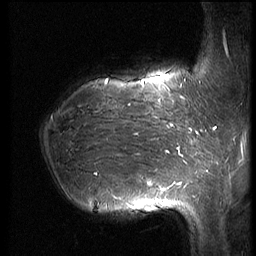
Breast MRI (dynamic contrast-enhanced), one sagittal slice; slice 20 of 66 in the series (ordered by position); dynamic contrast-enhanced series, image 2 of 3 at this slice position (ordered by acquisition); 1.5 T; TE 4.2 ms, TR 8.9 ms; 256 × 256 image matrix, field of view 200 × 200 mm. Patient: female, 39 years. From the clinical record (not read from this slice): setting: breast cancer imaged before/during neoadjuvant chemotherapy; receptor status: HER2-positive.
Outlined on this slice (semi-automatically segmented with operator editing):
- analysis volume of interest (the breast-tissue region the enhancement analysis was run in; not a lesion): bounding box (x1, y1, x2, y2) in pixels: (39, 75, 188, 218)
- tumour enhancement mask (voxels above the 140 % enhancement threshold inside the analysis volume of interest): (95, 80, 181, 206)